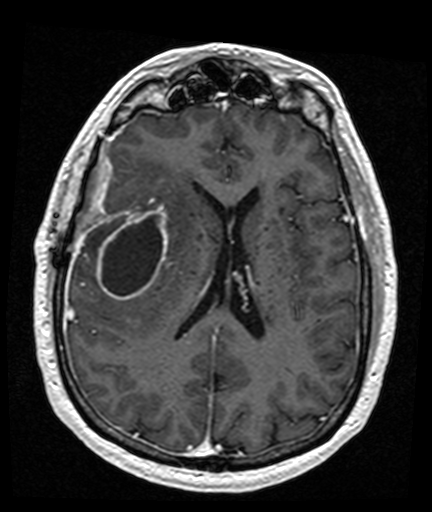
Brain MRI from a brain-tumour surgery series, one axial slice; position 70 of 176 along the scan axis; T1-weighted post-contrast; 1 mm slice thickness; 432 × 512 image matrix. Case-level facts recorded for this patient, not image findings: histopathology: Glioblastoma; WHO grade: 4; IDH mutation: no; tumour location: Right Frontal Temporal, Posterior Sylvian Fissure.
Outlined on this slice (expert manual segmentation):
- tumour: box from (x=97, y=207) to (x=170, y=301) px